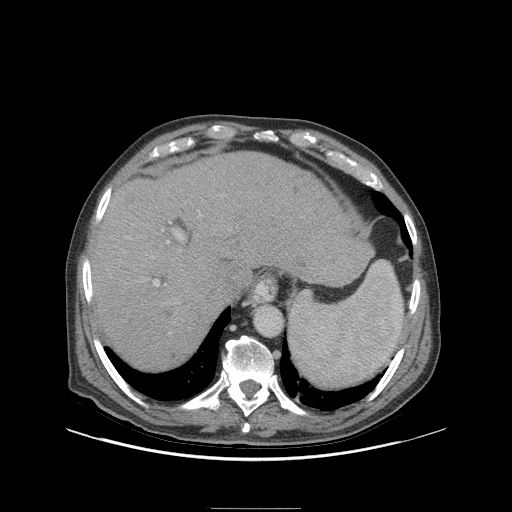
Contrast-enhanced abdominal CT (liver protocol), one axial slice. Position 77 of 105 along the scan axis. Soft-tissue window (W 400 / L 40 HU). 2.5 mm slice thickness. 512 × 512 image matrix. Case-level facts recorded for this patient, not image findings: diagnosis: hepatocellular carcinoma (patient treated with transarterial chemoembolisation; whether this scan precedes or follows treatment is not stated here); TNM stage (as recorded): Stage-I; Child-Pugh class: A; tumour nodularity: uninodular; tumour size: 5.1 cm.
Structures marked on this image (semi-automatically segmented with operator editing):
- abdominal aorta: bounding box [x1, y1, x2, y2] px = [254, 306, 282, 336]
- liver parenchyma outside the tumour (the mass and vessels are separate outlines, so this box may not span the whole liver): [91, 152, 360, 370]
- liver vessels: [153, 231, 184, 287]